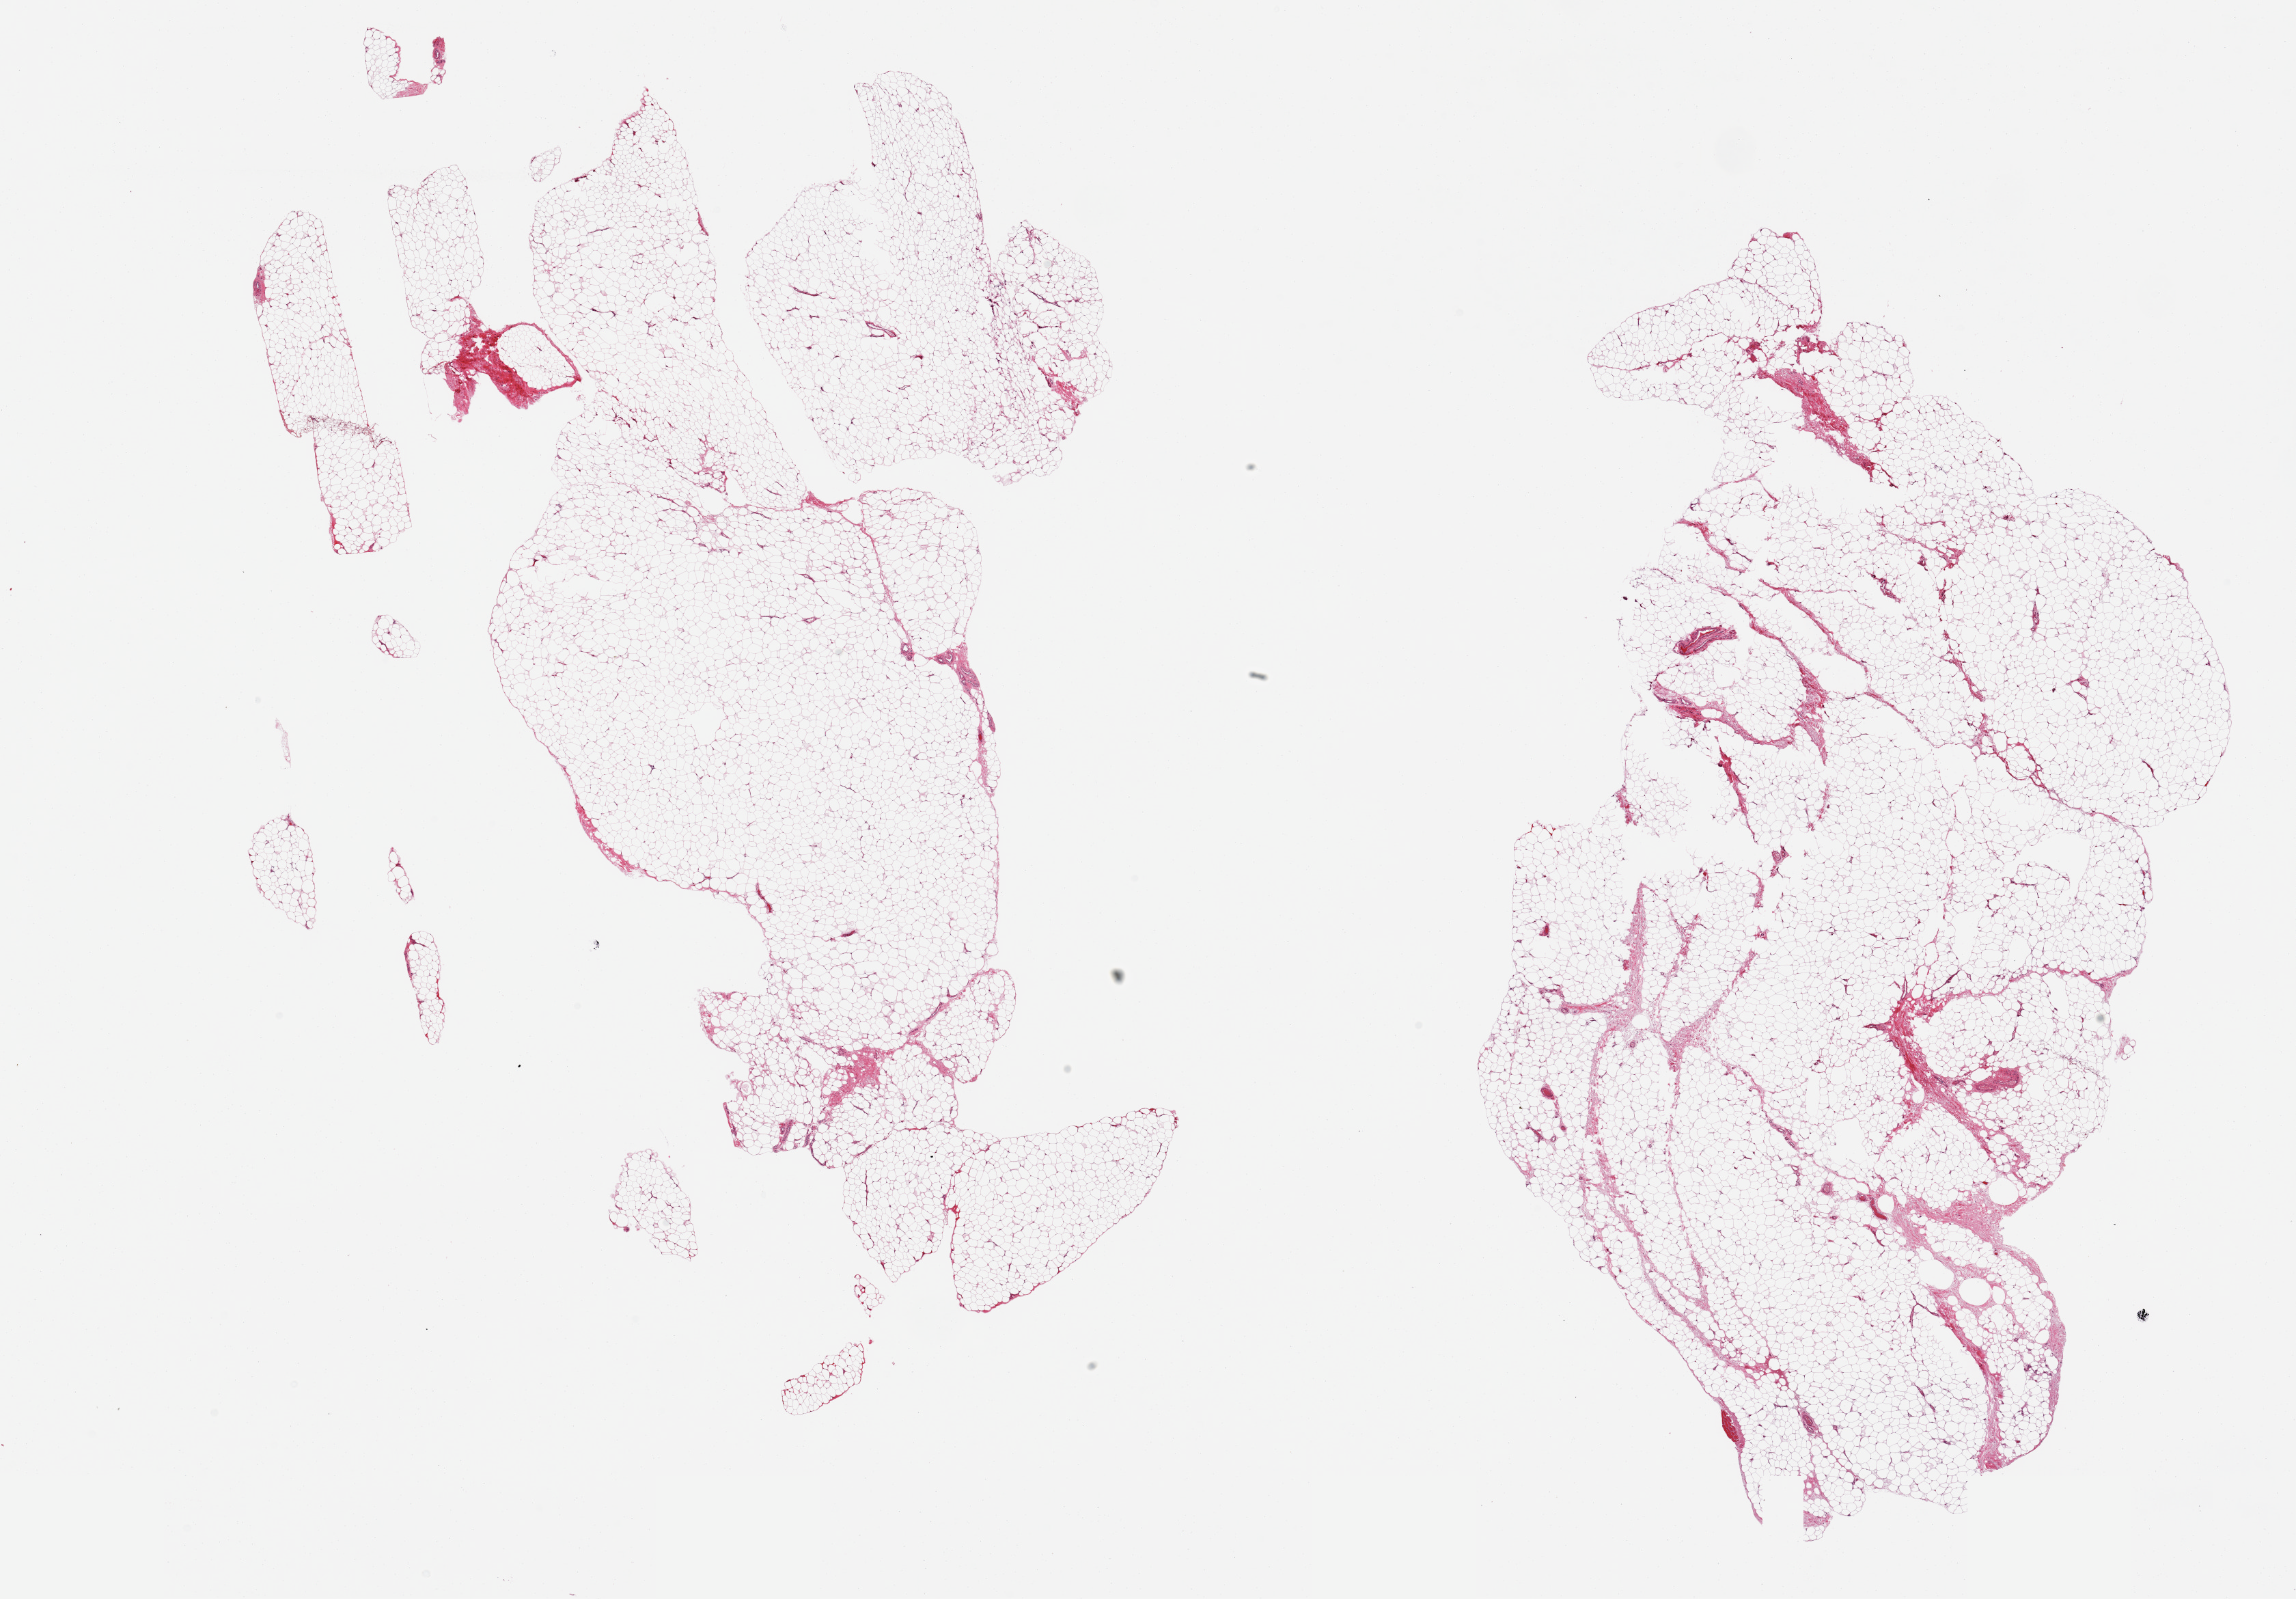
Digitized H&E-stained section — a low-resolution overview of the entire scanned area, about 26.6 x 18.5 mm (from a 20x scan). PAXgene-fixed, paraffin-embedded tissue. Sampled site (target tissue): adipose tissue. Tissue donor sample. Donor sex: male.
- reviewer comment on this tissue sample: 2 pieces; ~10% of fibrovascular component